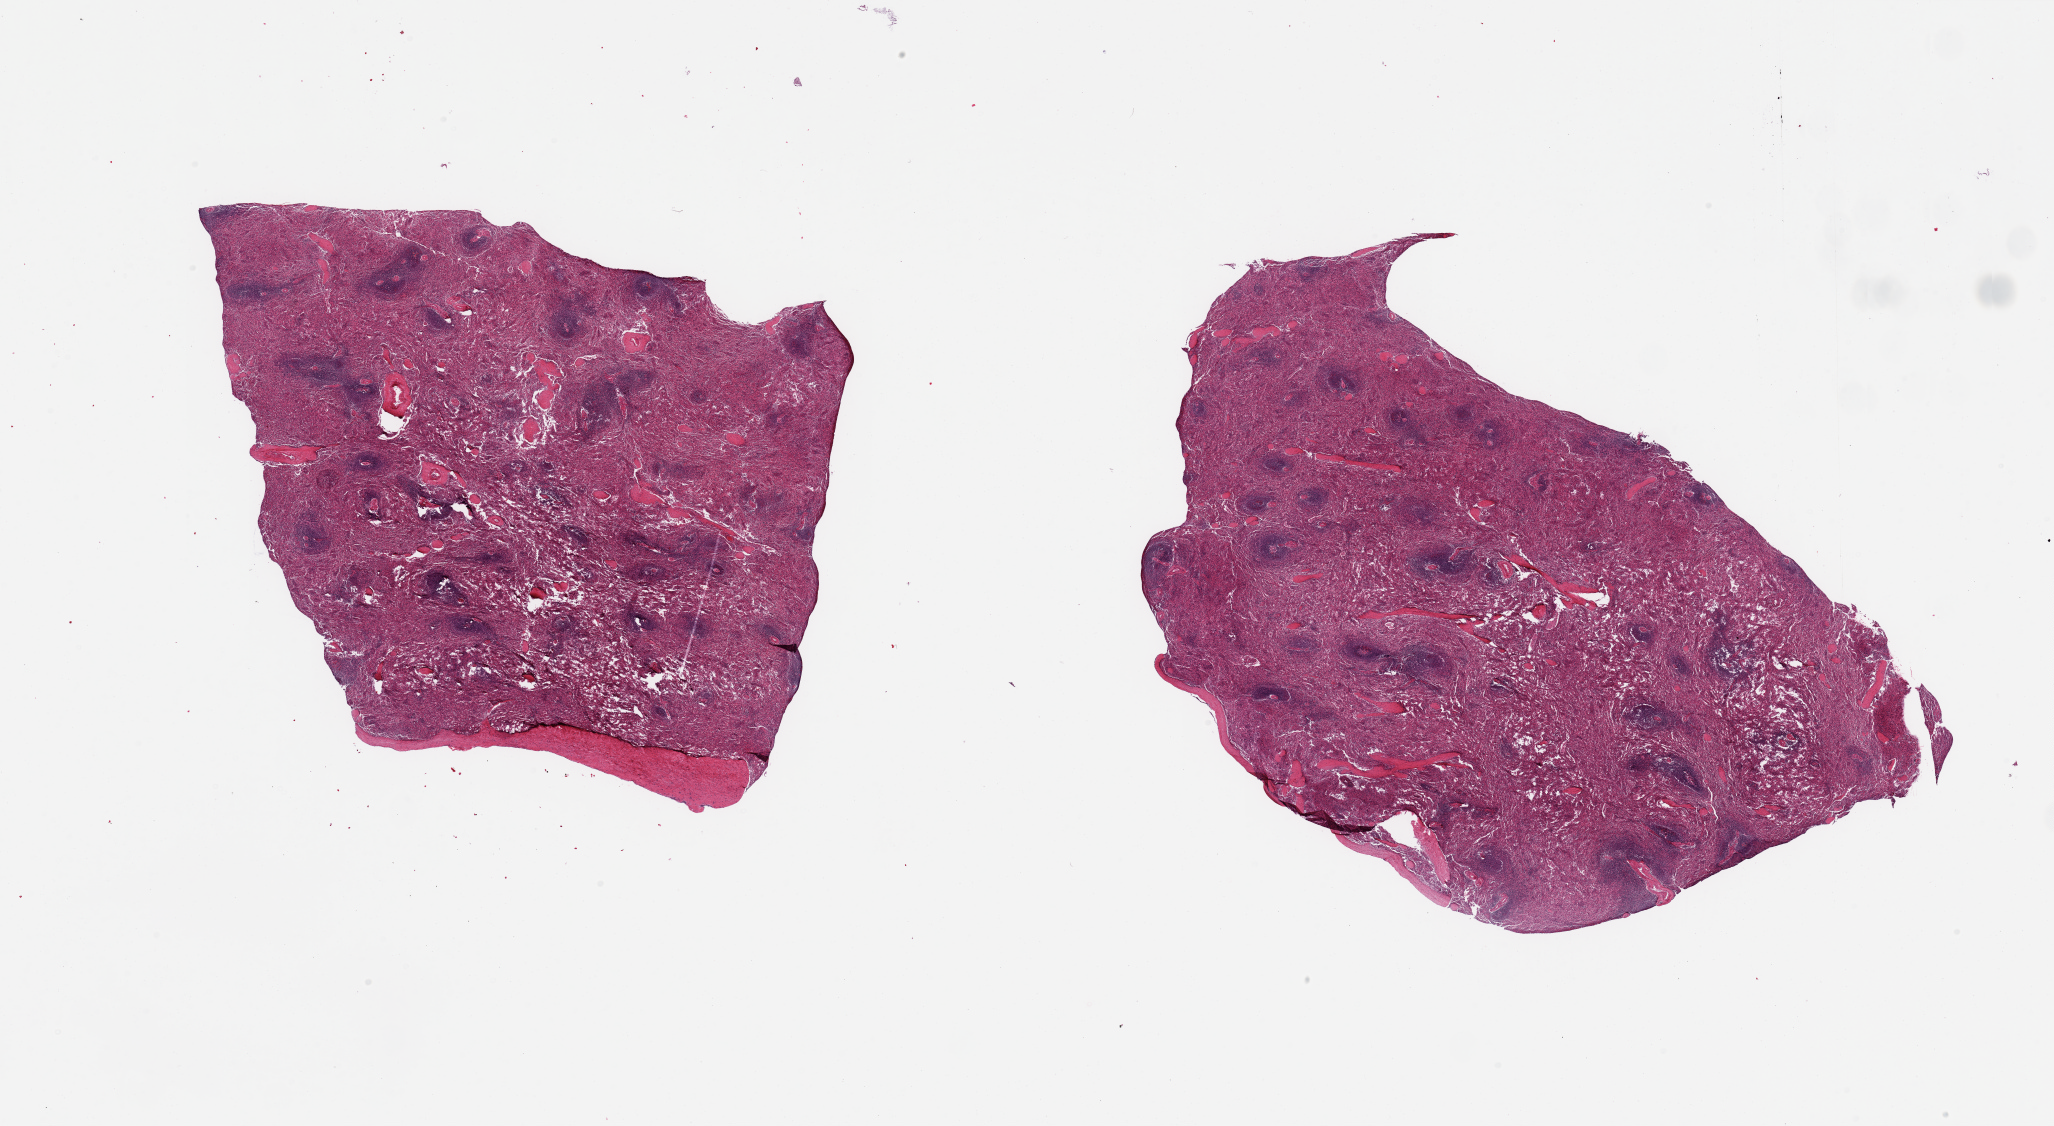
Haematoxylin and eosin whole-slide image, low-resolution overview of the scanned area, about 32.5 x 17.8 mm (from a 20x scan); PAXgene-fixed paraffin-embedded (PFPE) section; sampled site (target tissue): spleen; donor tissue sample. Donor: female.
• reviewer comment on this tissue sample: 2 partly fragmented pieces; capsule present on 1 edge